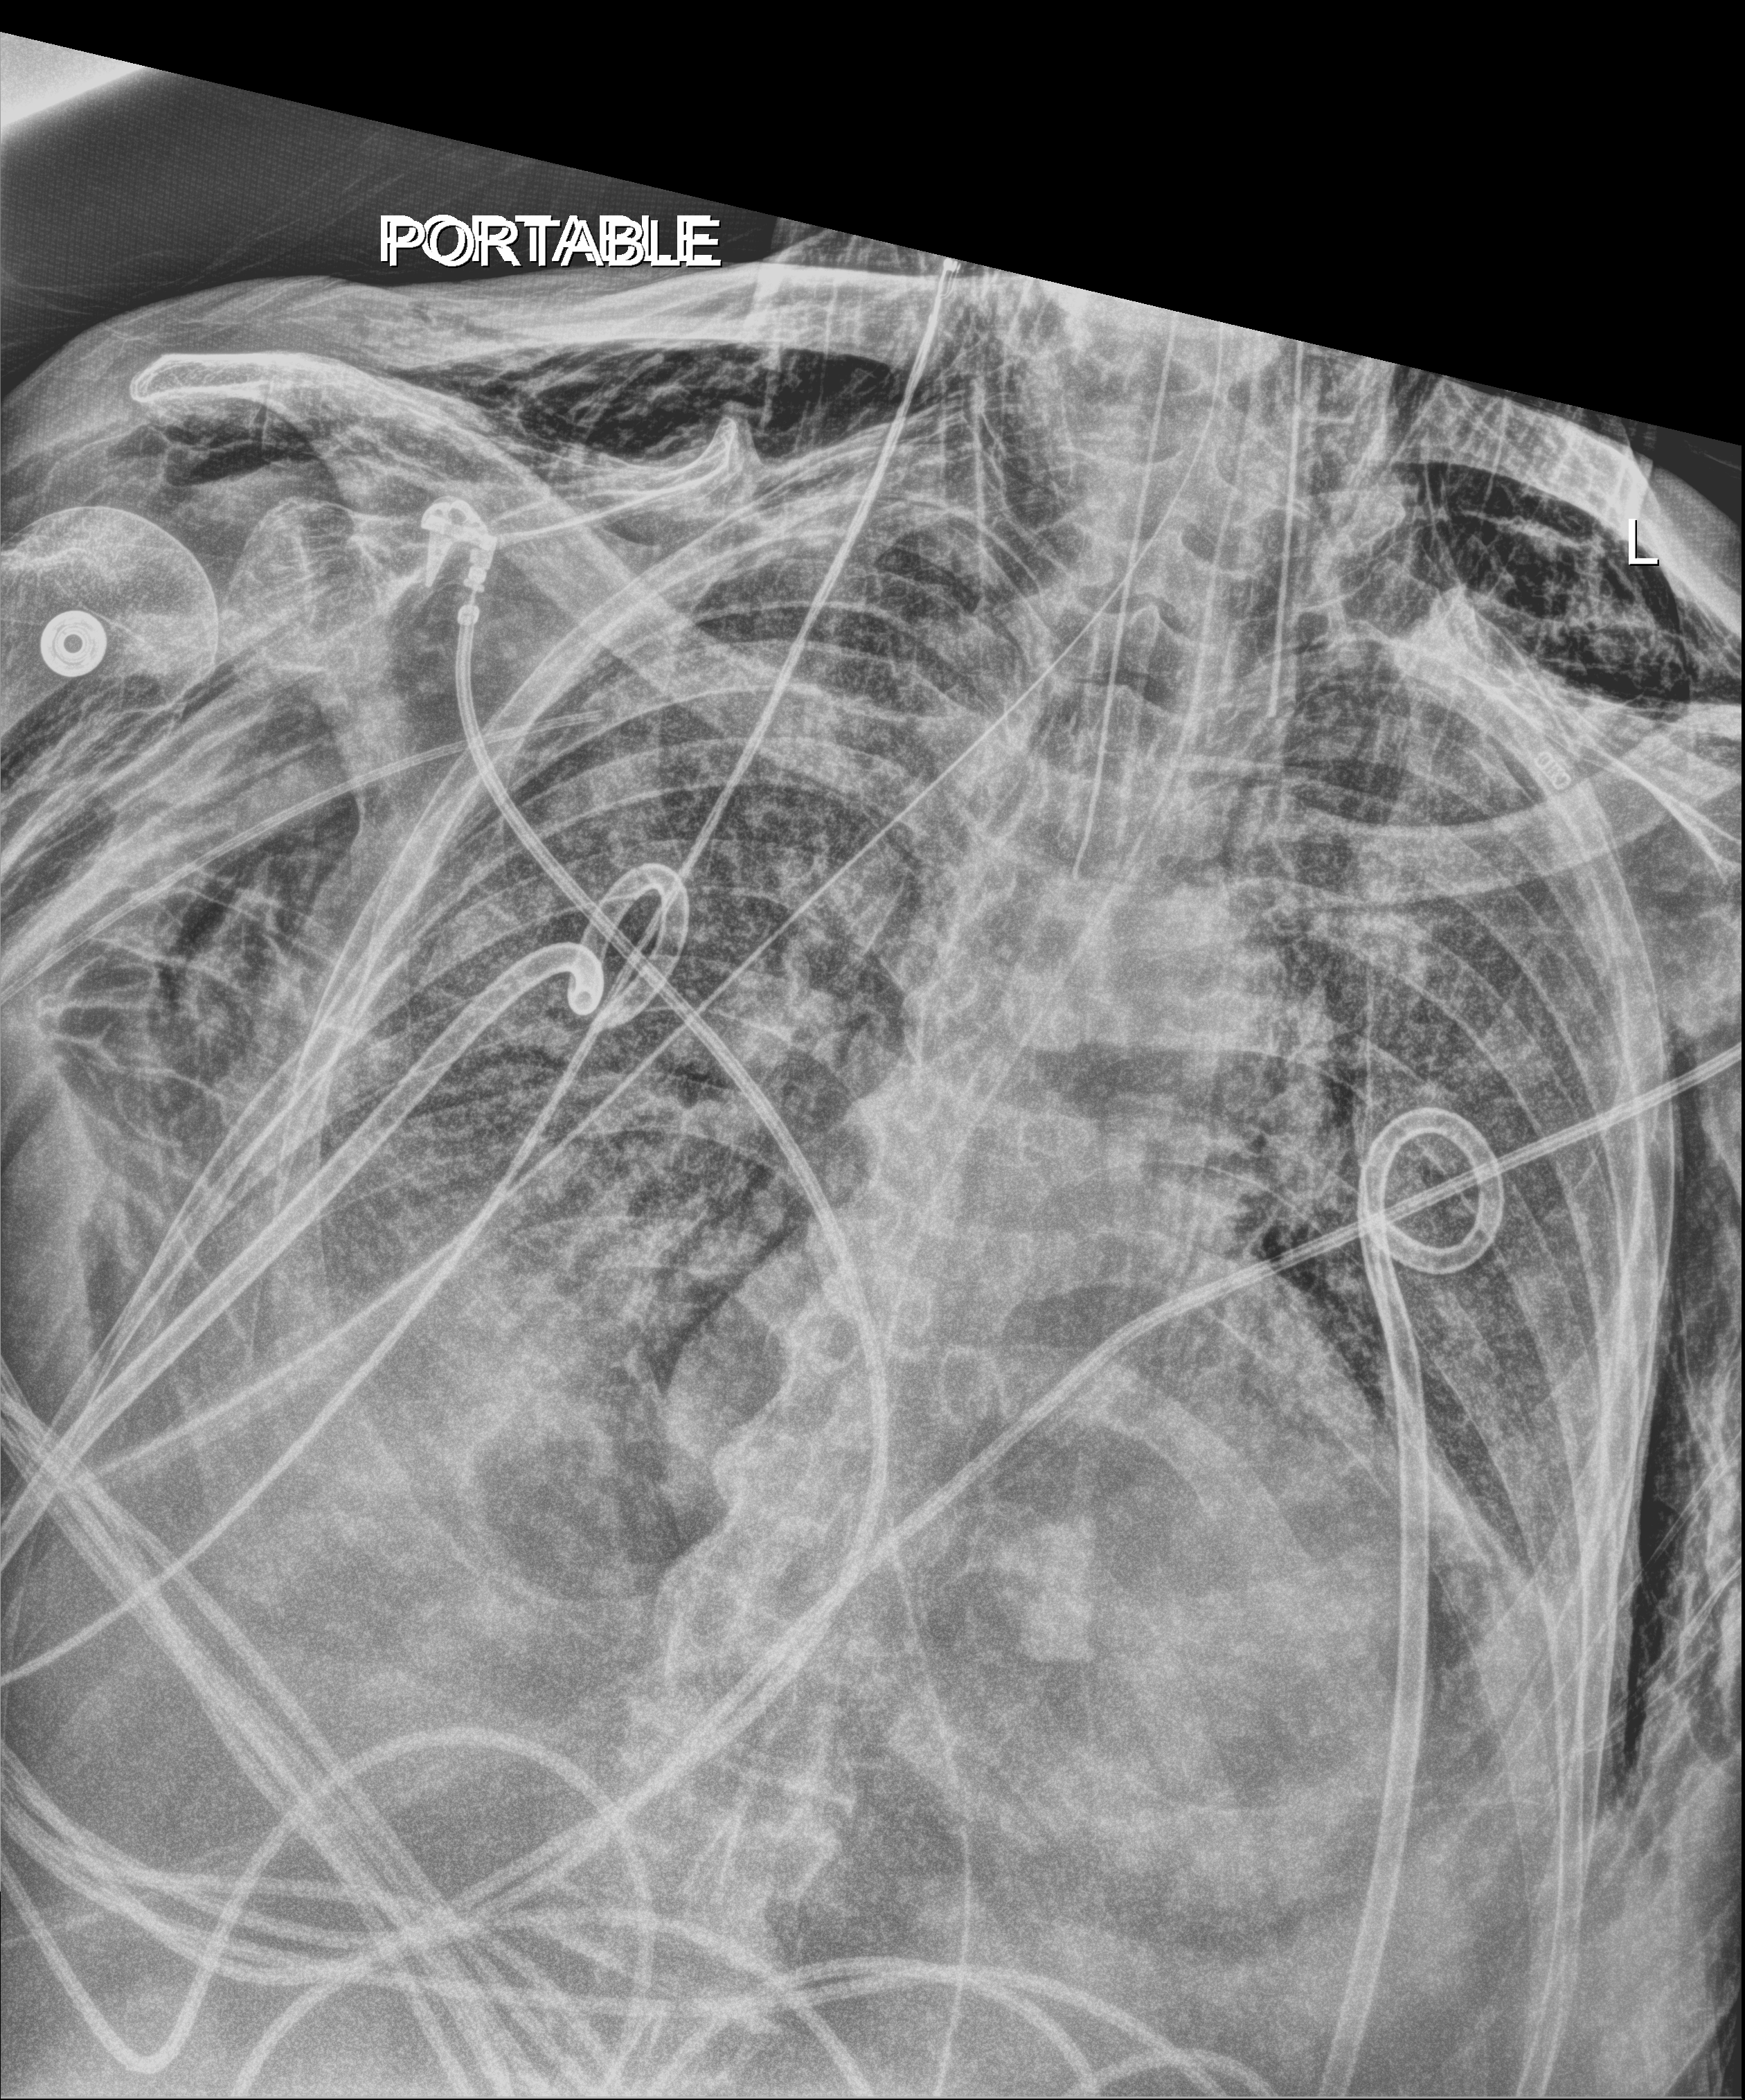
Bedside chest radiograph (digital radiography), anteroposterior (AP) projection. Patient hospitalised with COVID-19; male, aged 75–90 years.
Hospital-stay facts (about this admission, not read from this image; timing relative to this image not recorded):
- COPD (admission record): no